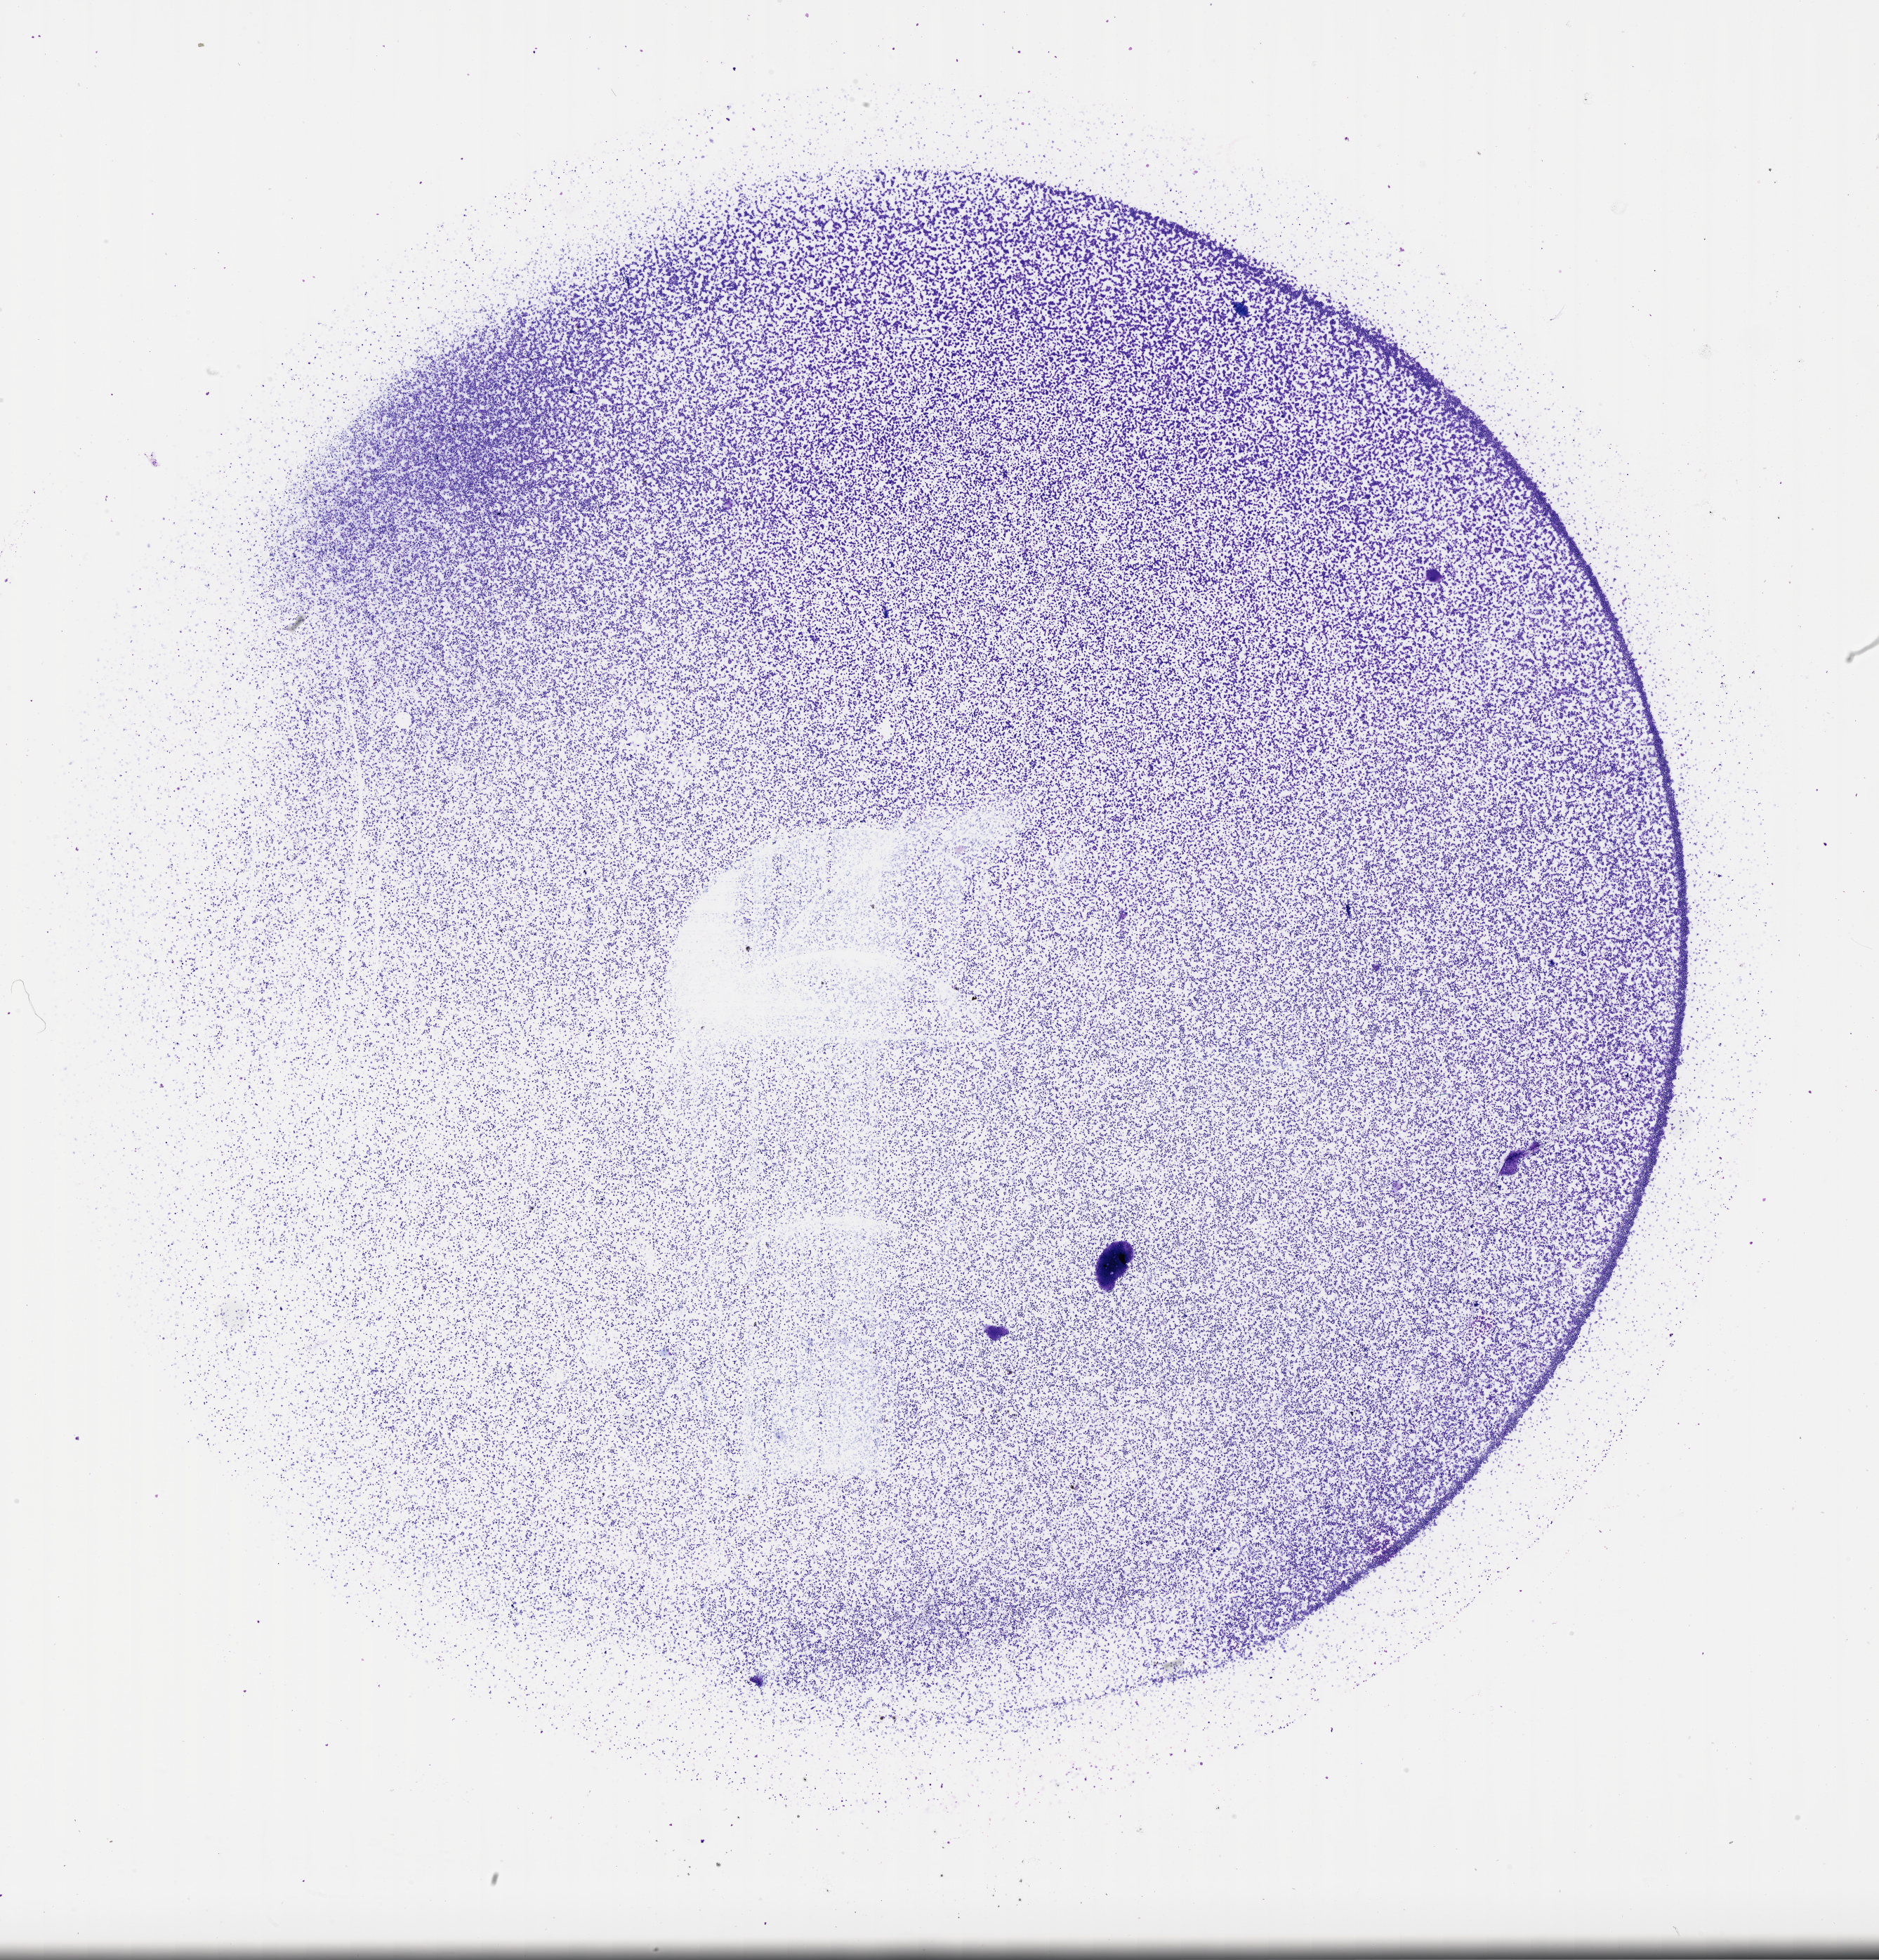
H&E-stained whole-slide image, low-resolution overview of the scanned area, about 21.6 x 22.5 mm; bone marrow (leukaemic) sample. Patient: female, age 57 years. Blasts: 50%.
Diagnosis: Acute Myeloid Leukemia. WHO classification: Acute Promyelocytic Leukemia with t(15;17)(q22;q12); PML-RARA. FAB classification: M3.